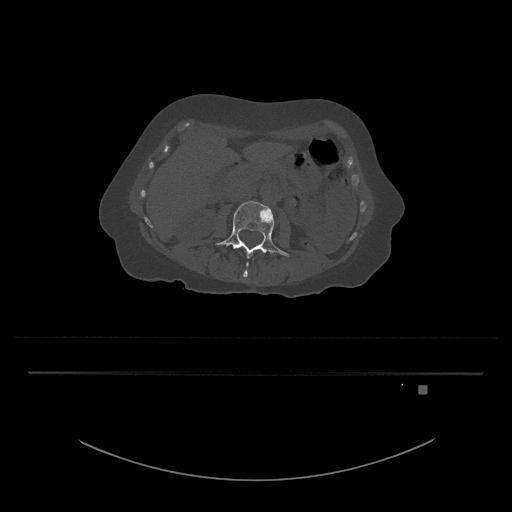
CT including the spine, one axial slice. Slice 433 of 797 in the series (ordered by position). Reconstruction kernel Br40s/3. Bone window (W 1800 / L 400 HU). 0.5 mm slice thickness. 512 × 512 image matrix. Patient: female, 57 years. From the clinical record (not read from this slice): primary cancer: cervical.
Outlined on this slice (semi-automatic segmentation, software-assisted and operator-edited):
- L3 vertebra: box from (x=216, y=201) to (x=290, y=278) px